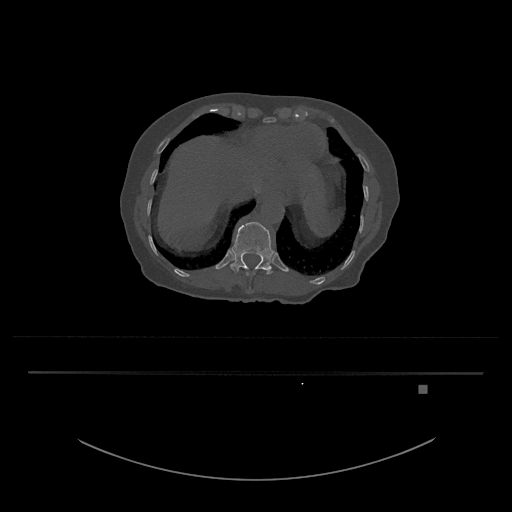
CT including the spine, one axial slice. Position 627 of 797 along the scan axis. Reconstruction kernel Br40s/3. 120 kVp. Bone window (W 1800 / L 400 HU). 512 × 512 image matrix, field of view 500 × 500 mm. Patient: female, 57 years. From the clinical record (not read from this slice): primary cancer: cervical.
Annotated regions visible in this slice (semi-automatically segmented with operator editing):
- T11 vertebra: box from (x=246, y=272) to (x=255, y=275) px
- T12 vertebra: (x=230, y=222)–(x=274, y=274)